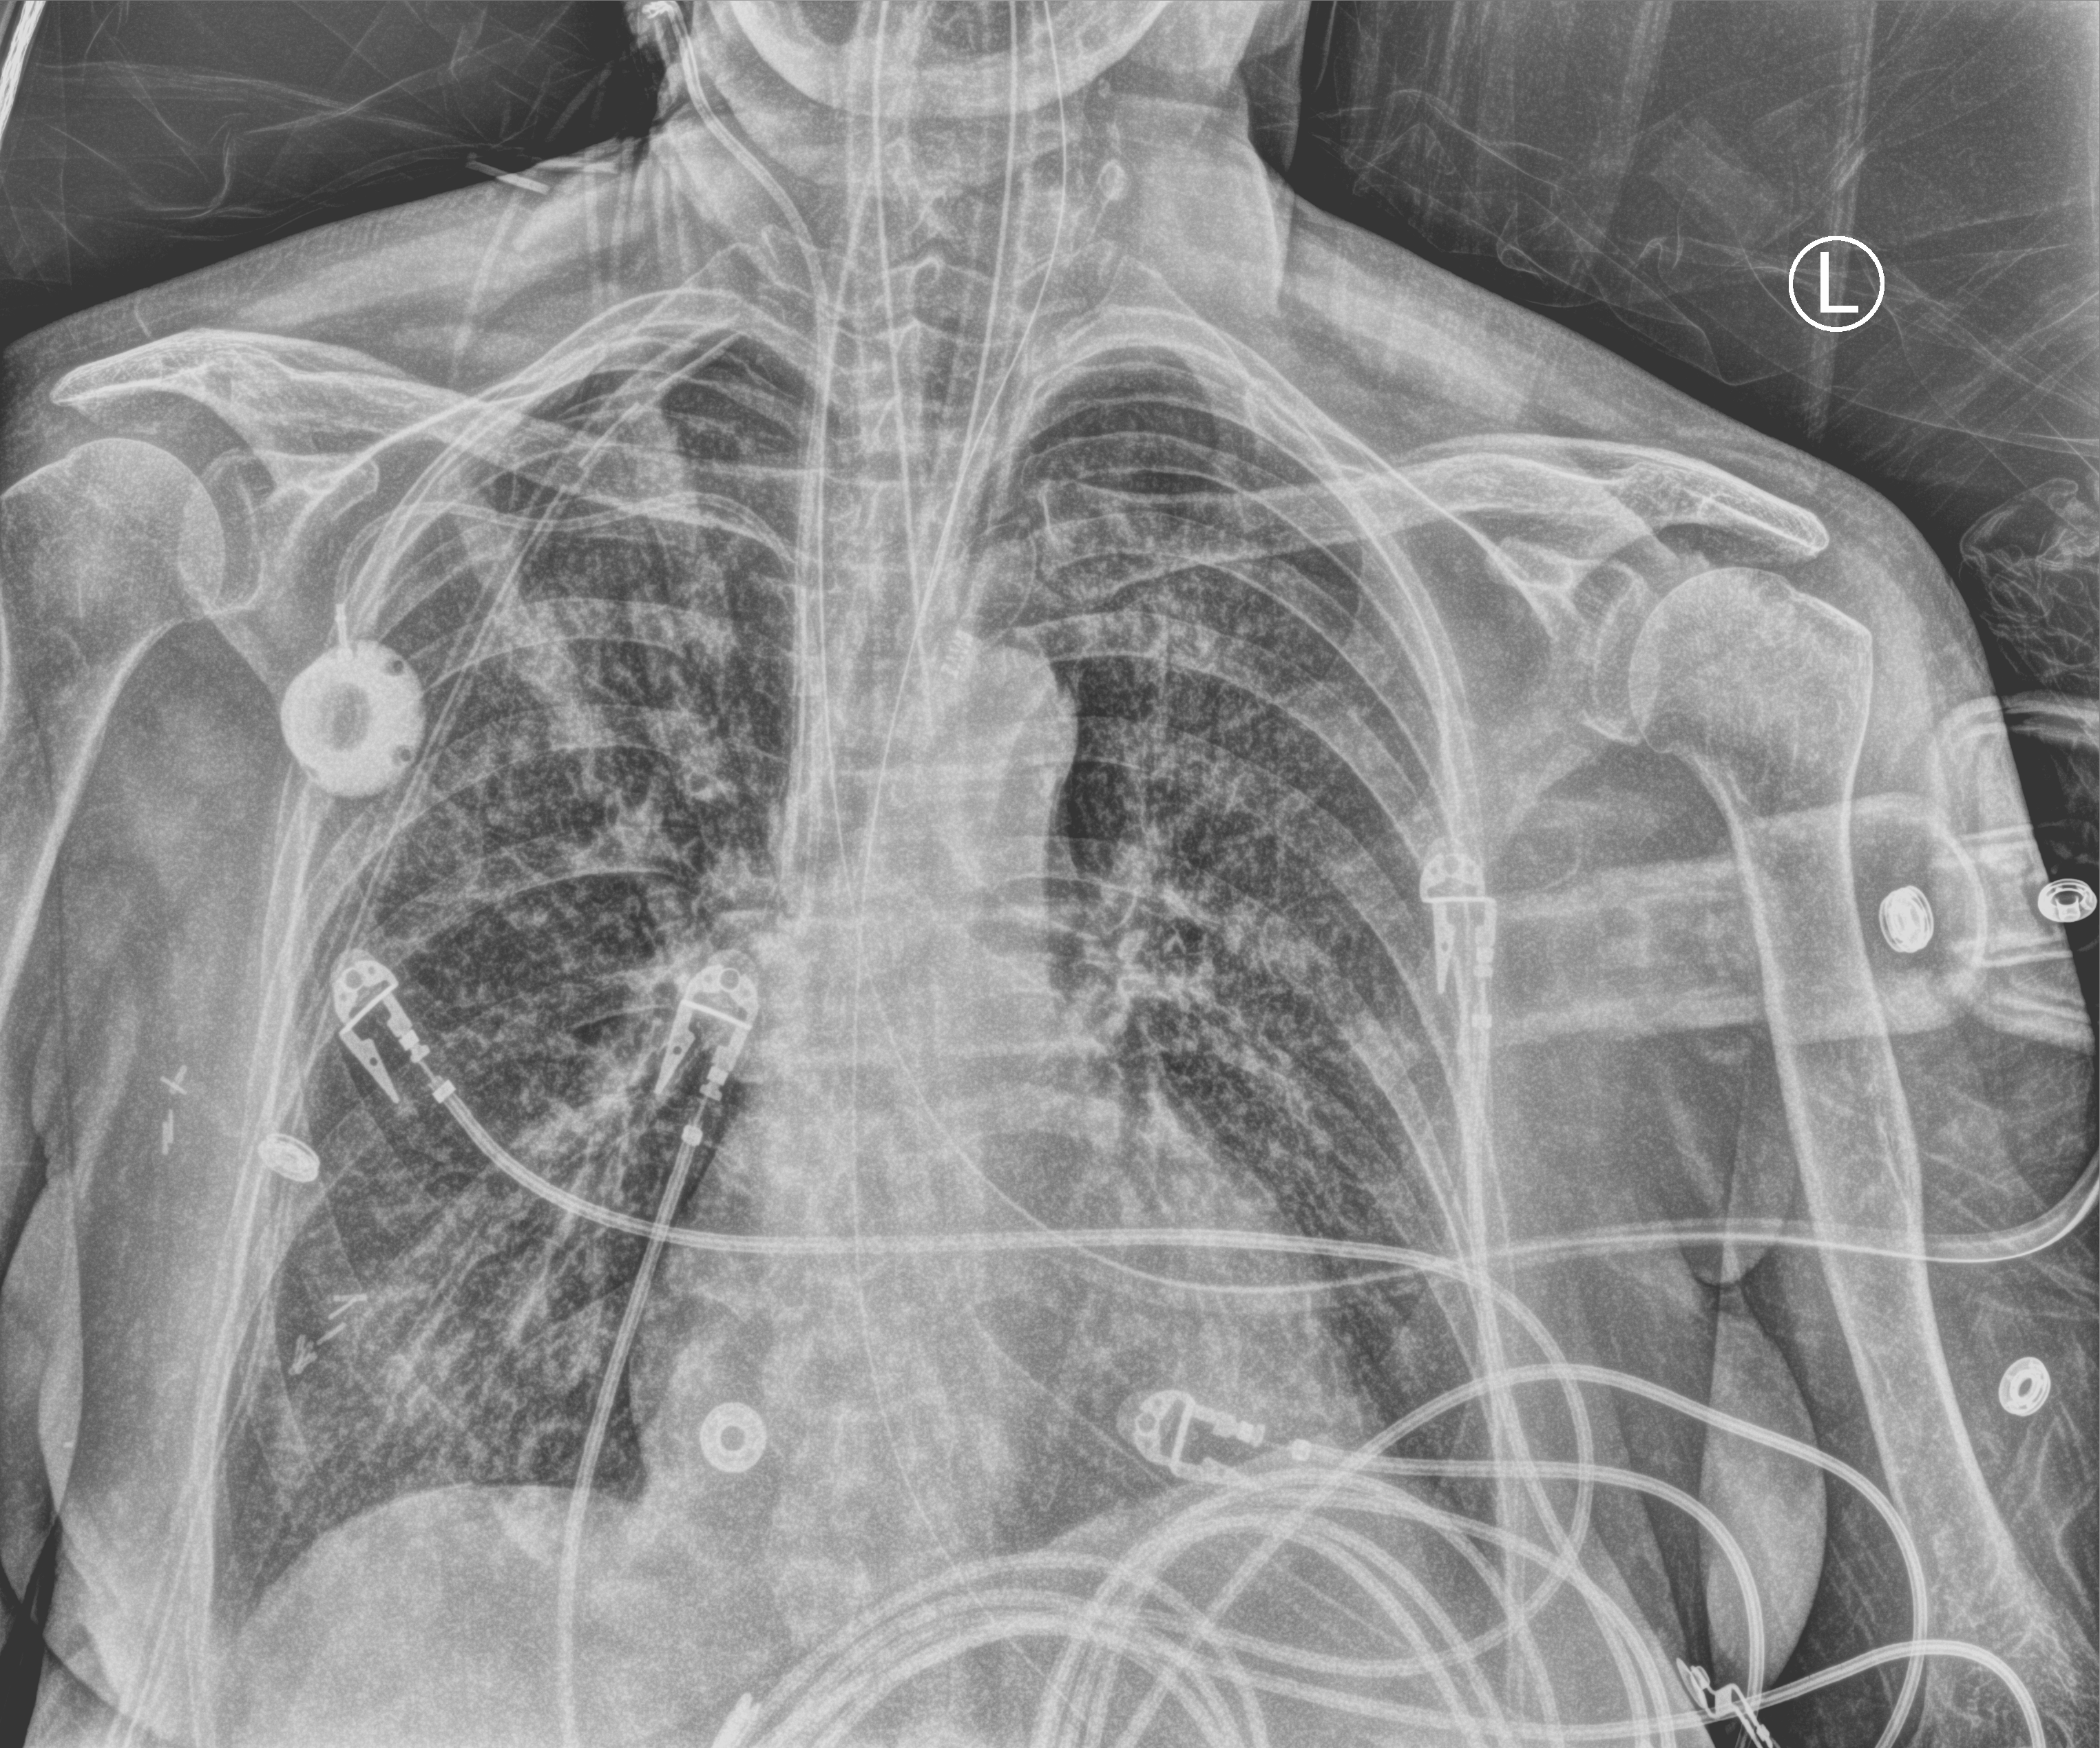
Chest X-ray (portable), anteroposterior (AP) projection. Patient hospitalised with COVID-19; female, aged 60–74 years.
Admission-level facts for this patient (not findings on this image; timing relative to this image not recorded):
- mechanically ventilated during this hospital stay: yes